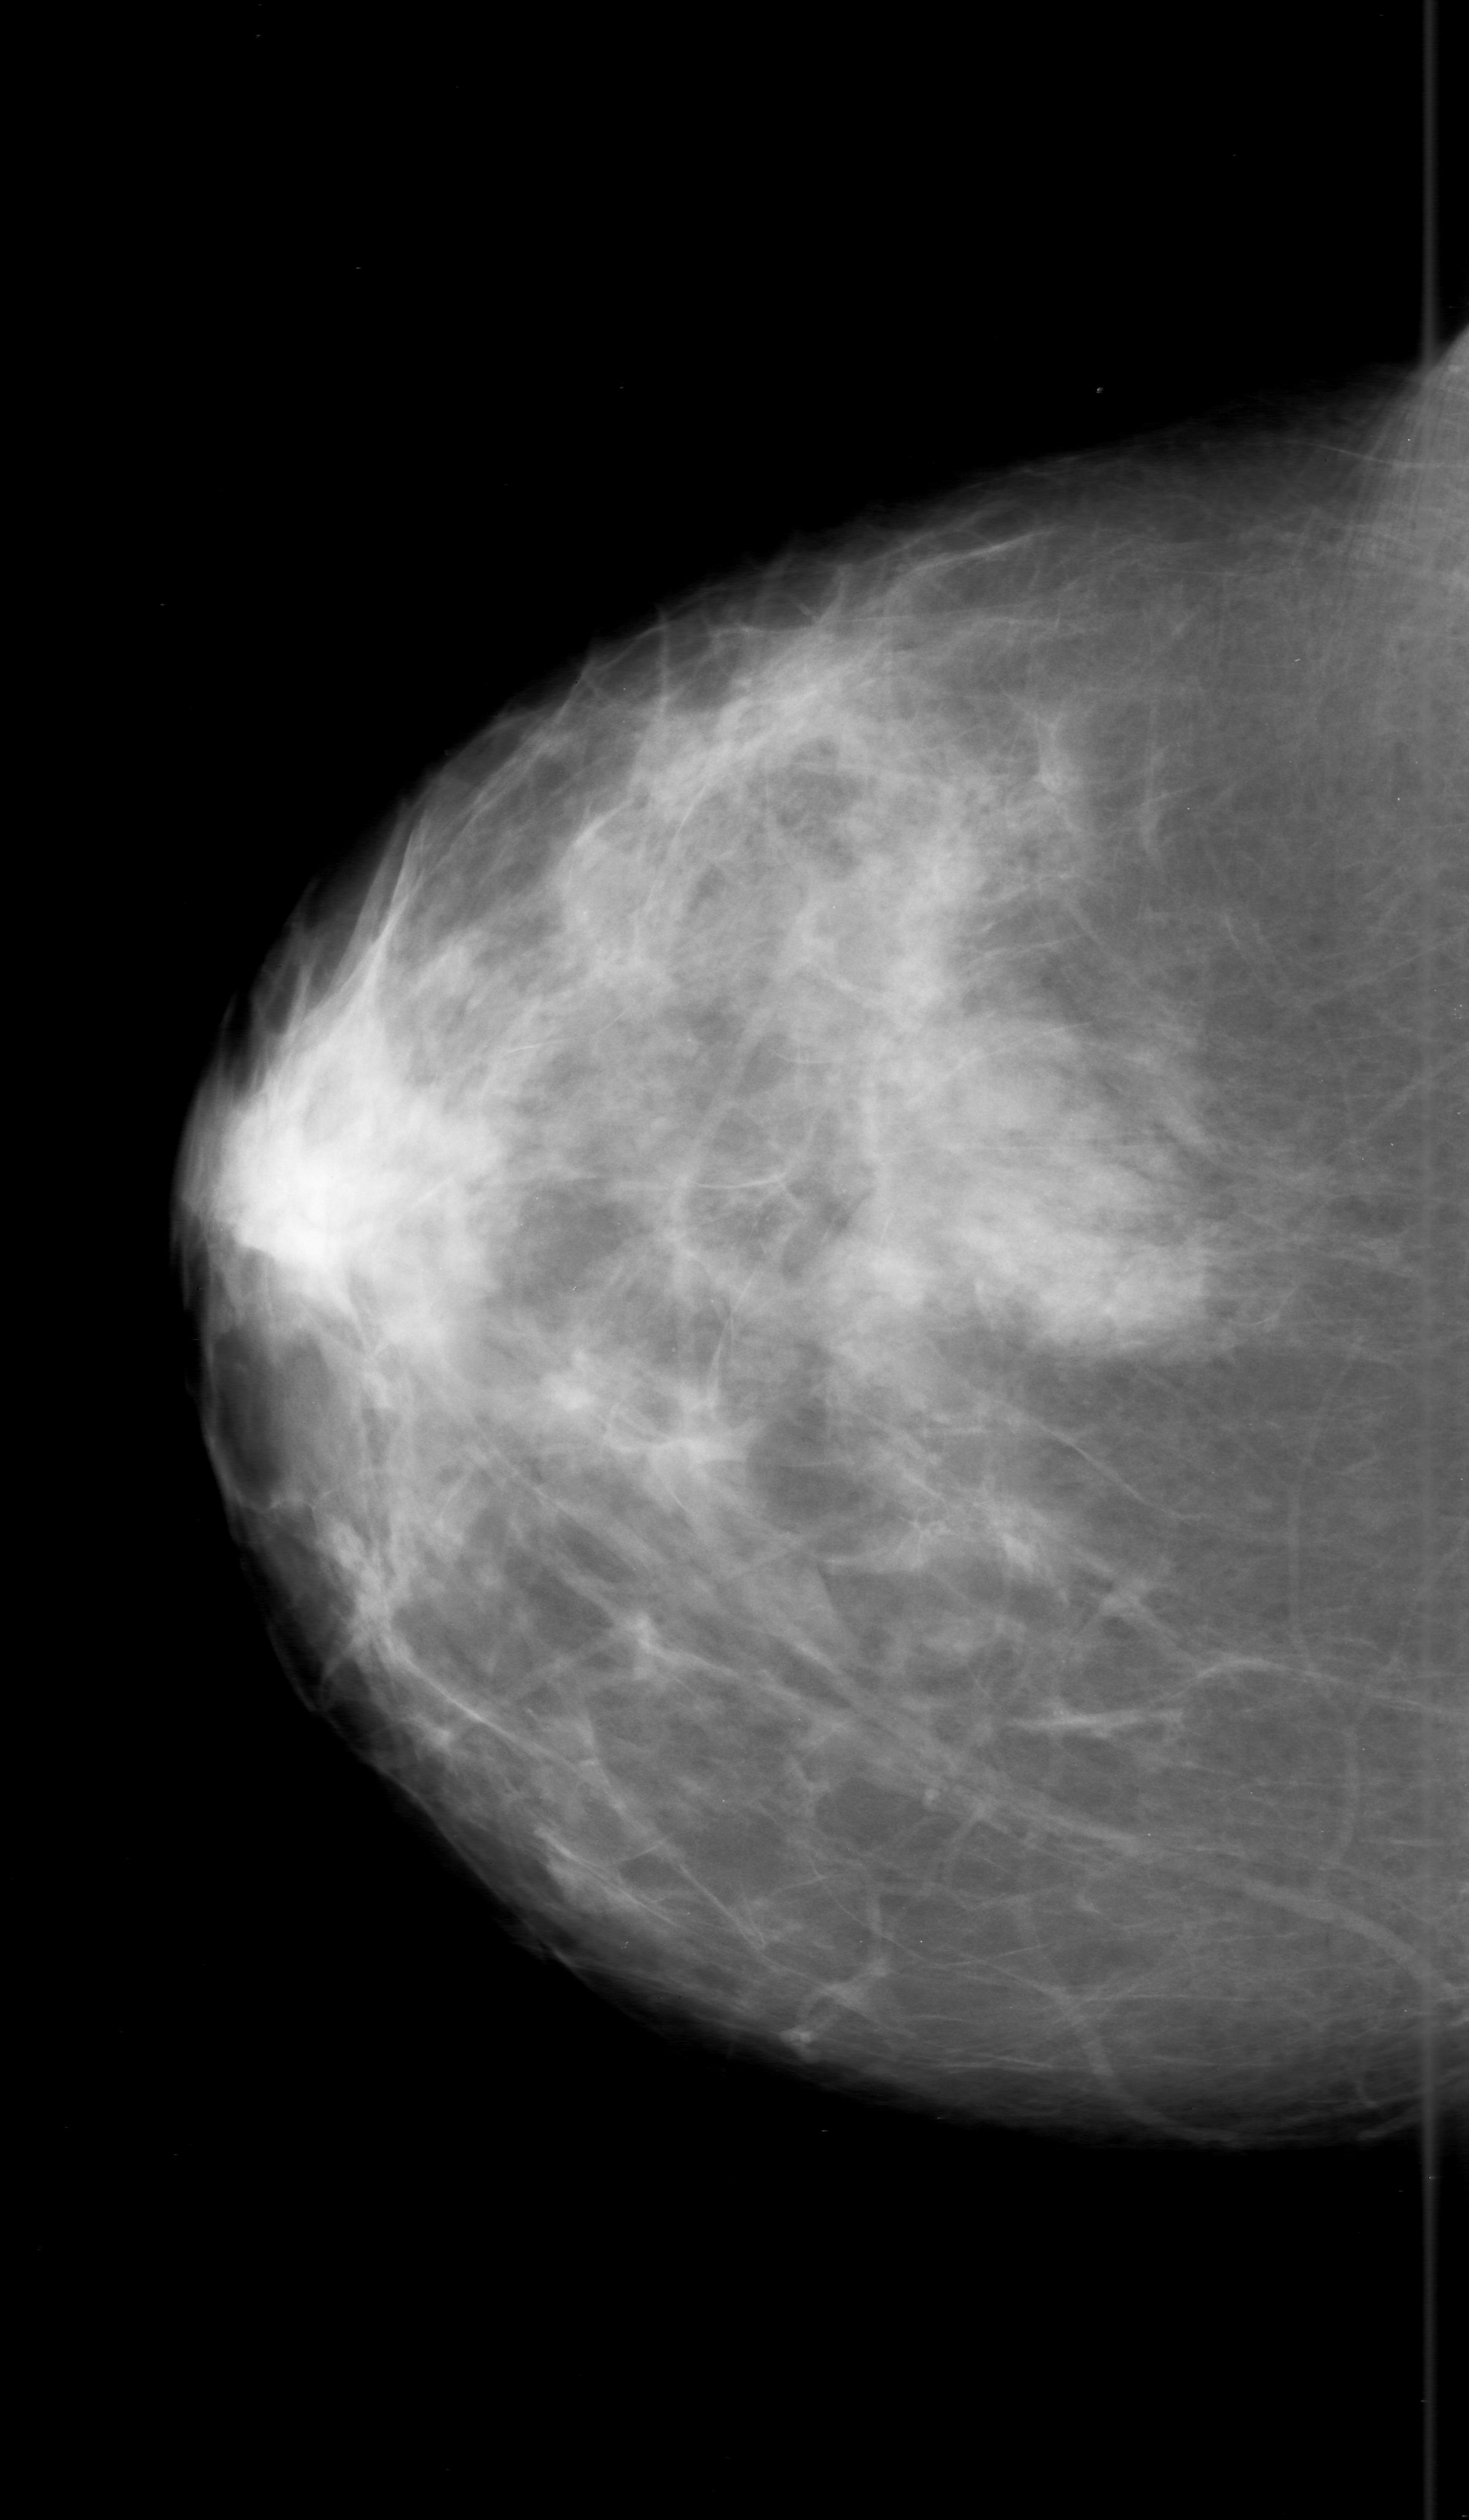
Digitized screen-film mammogram; right breast; CC view; BI-RADS breast density category 2 (scale 1–4); 1469 × 2520 image matrix.
Expert-marked regions of interest on this film, with their recorded descriptors:
- calcifications, morphology punctate, distribution clustered; BI-RADS assessment category 0; subtlety rating 2 on a 1 (subtle) to 5 (obvious) scale; pathology result (as recorded, not read from the image): benign: box from (x=984, y=1631) to (x=1185, y=1810) px